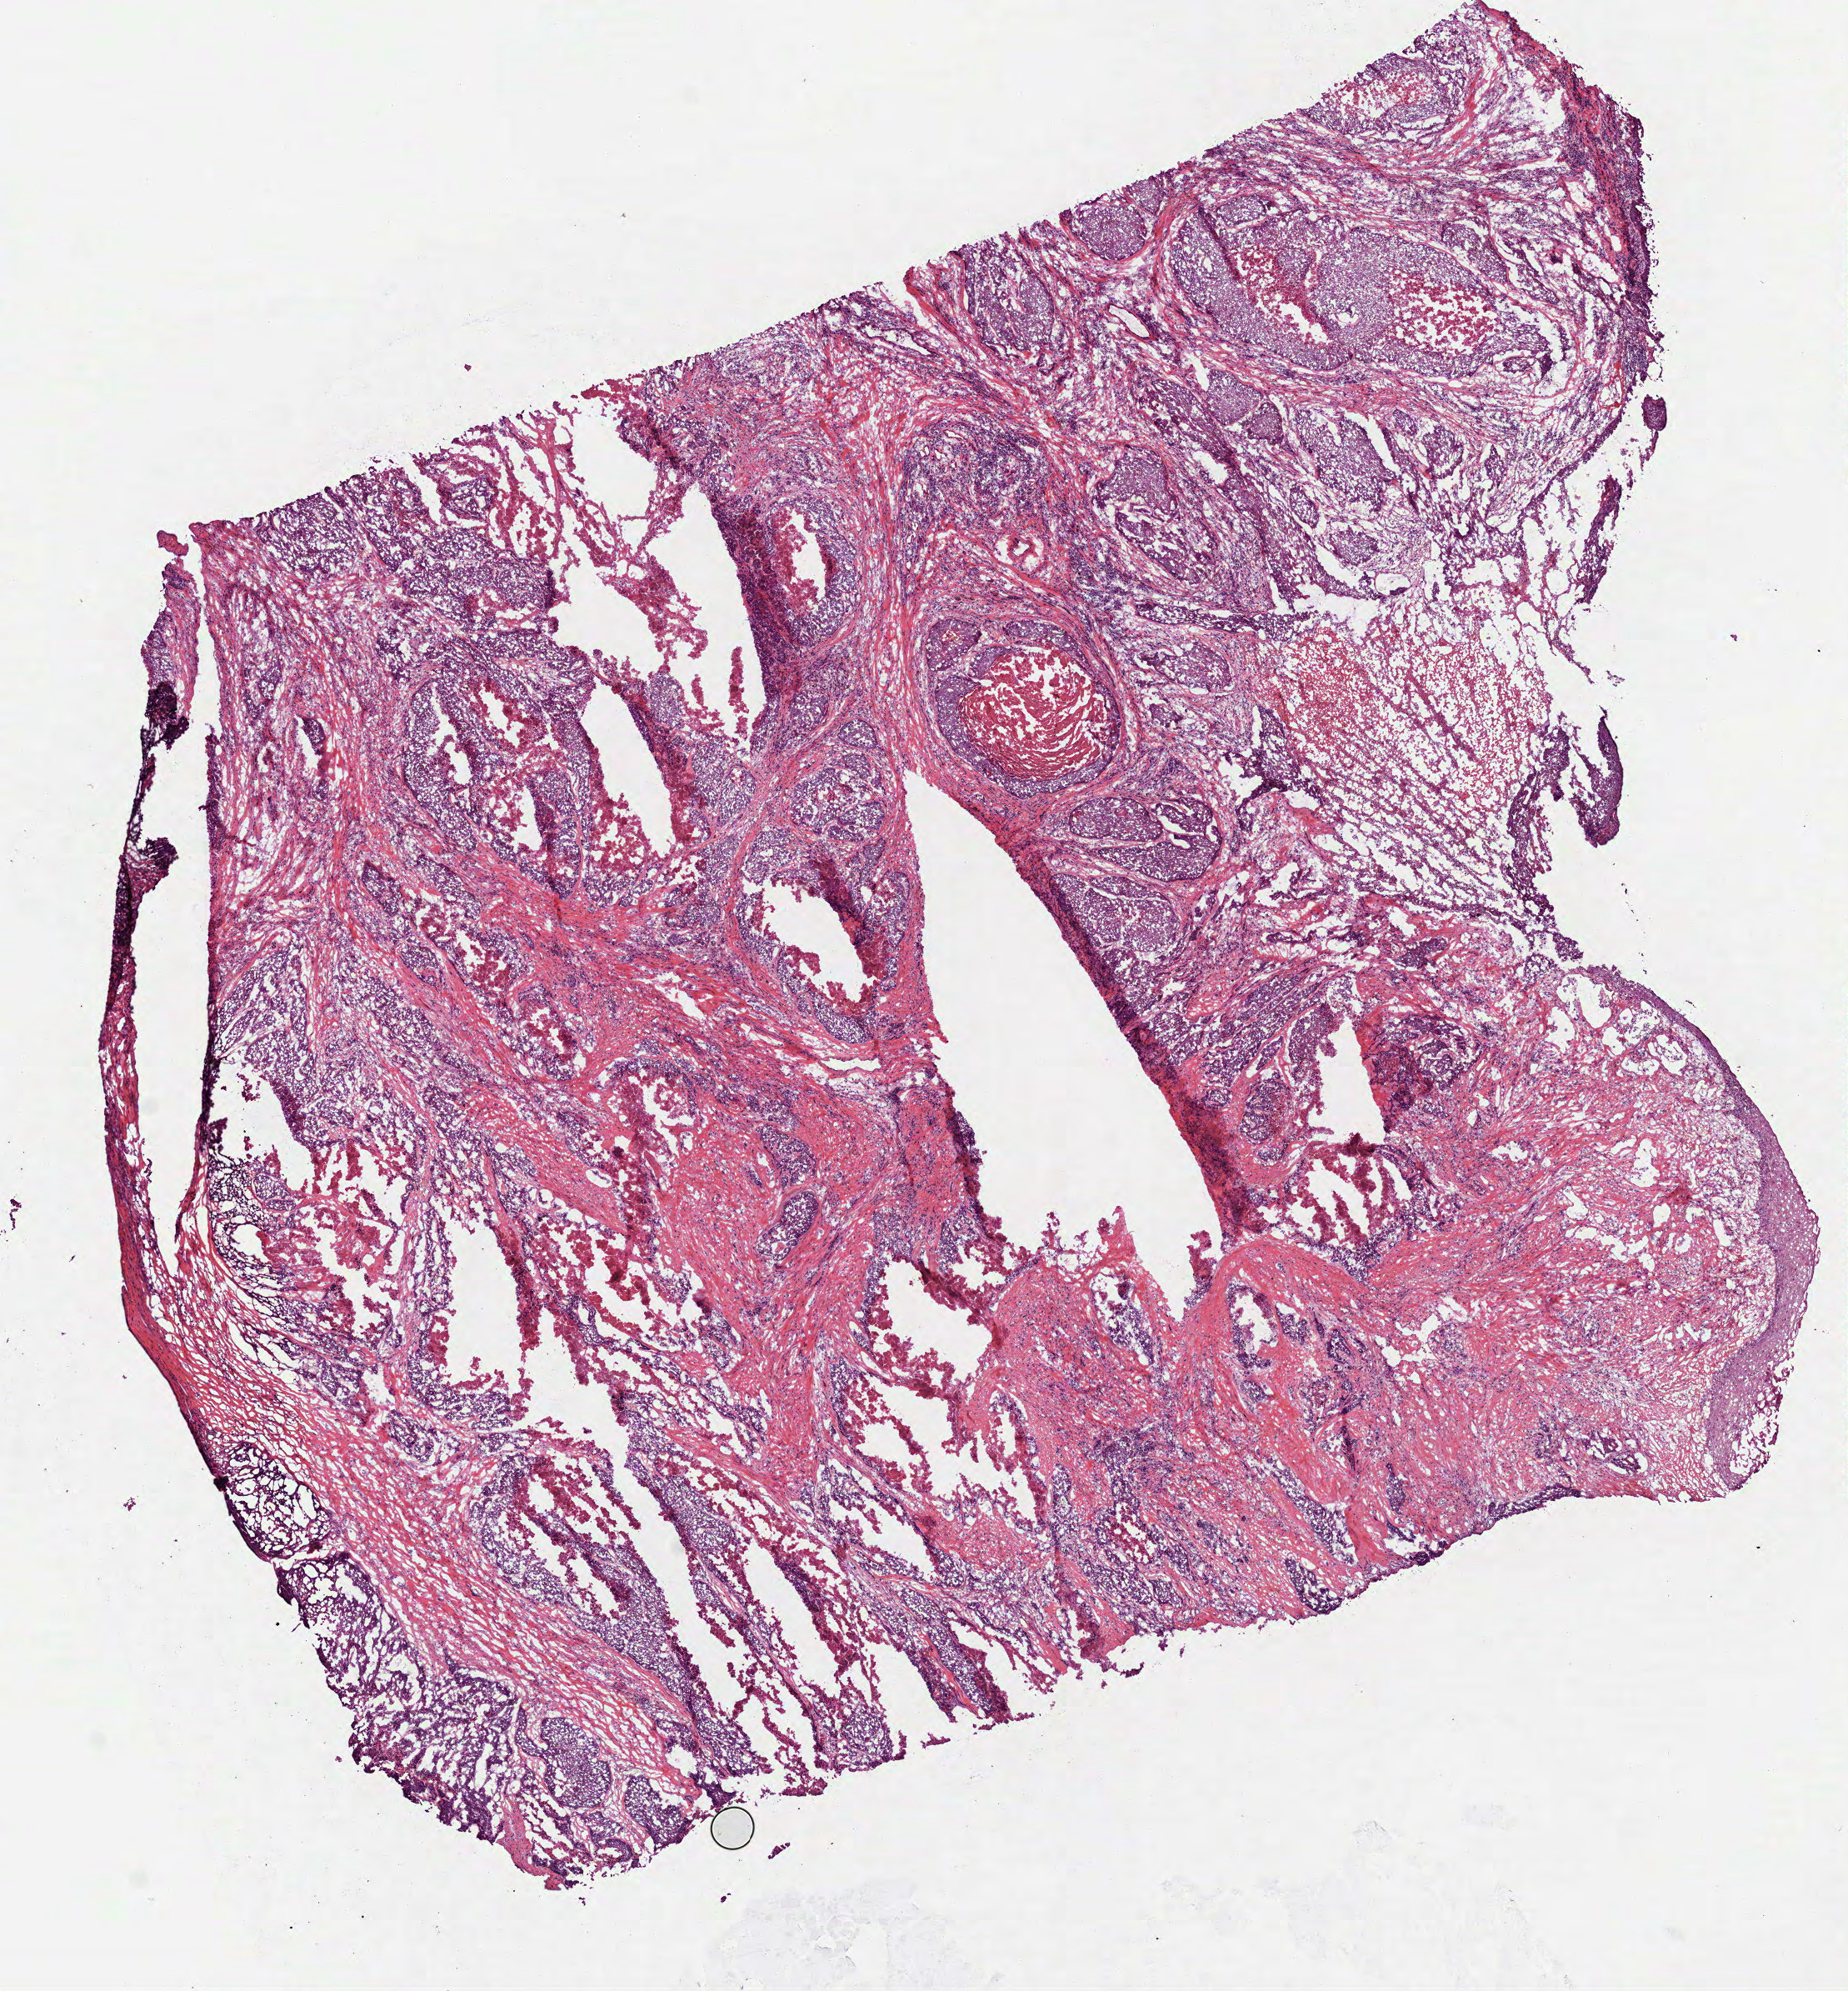
Digitized H&E tissue section (whole slide), shown as a low-resolution overview of the whole scanned area (about 8.9 x 9.6 mm); frozen section; sample: primary tumour, head and neck. Patient: male, age at initial diagnosis 65 years. Histologic grade: G2 (moderately differentiated). Pathologist review of this section (percent, as recorded): tumour cells 72%, tumour nuclei 65%, normal cells 0%, stromal cells 7%, necrosis 21%. Inflammatory infiltration, as recorded: lymphocyte infiltration 20%, monocyte infiltration 1%, neutrophil infiltration 2%.
• AJCC pathologic stage: IVA (7th edition)
• histologic diagnosis: Squamous cell carcinoma, NOS (larynx, NOS)